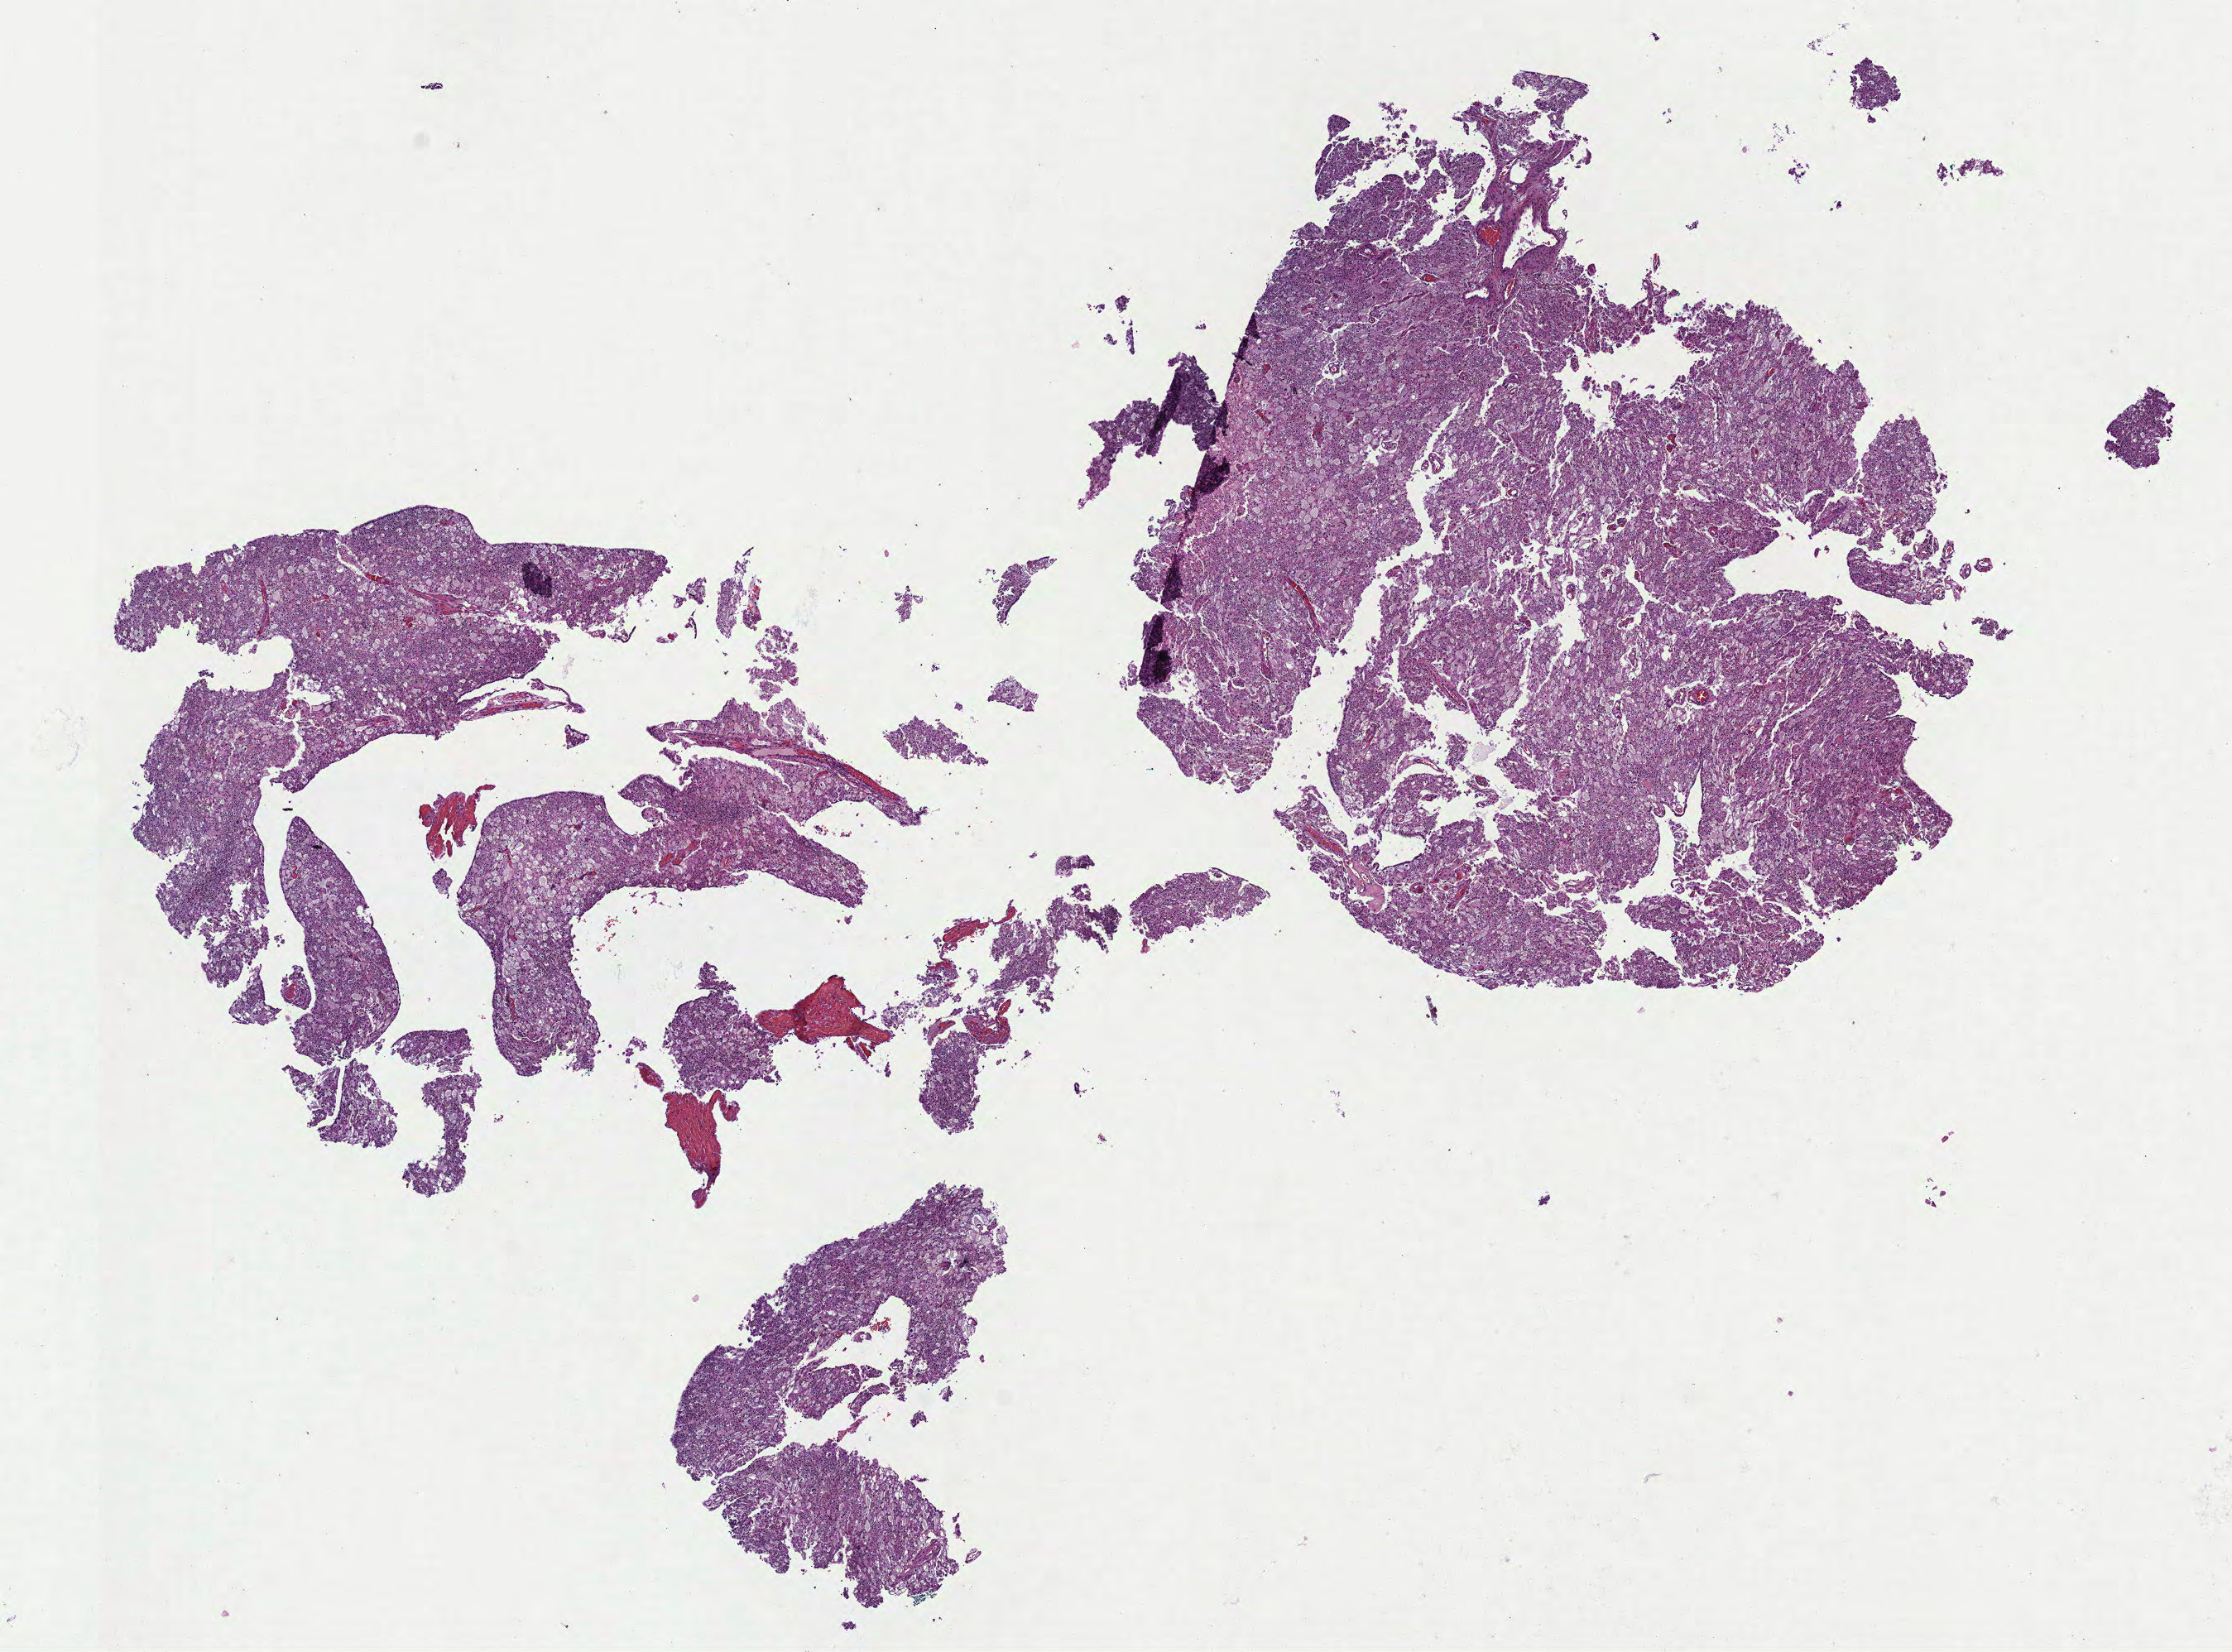
Whole-slide histology image, Hematoxylin and eosin (H&E) stained, shown as a low-resolution overview of the whole scanned area (about 10.9 x 8.1 mm). Formalin-fixed paraffin-embedded (FFPE) diagnostic section. Kidney, primary tumour sample. Female, age 50 years at initial diagnosis.
* histologic diagnosis: Renal cell carcinoma, chromophobe type
* AJCC pathologic stage: II